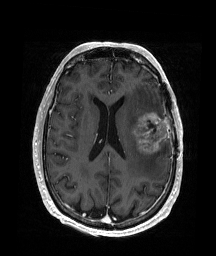
Brain MRI from a brain-tumour surgery series, one axial slice. Slice 79 of 176 in the series (ordered by position). T1-weighted post-contrast. 1 mm slice thickness. 216 × 256 image matrix, field of view 219 × 260 mm. From the clinical record (not read from this slice): histopathology: Glioblastoma; WHO grade: 4; IDH mutation: no; tumour location: Left Frontal.
Structures marked on this image (manually delineated by an expert):
- tumour: bounding box (x1, y1, x2, y2) in pixels: (131, 112, 169, 155)